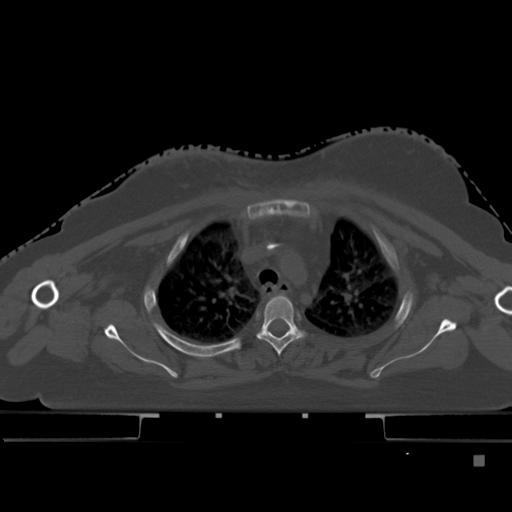
CT including the spine, one axial slice. Position 346 of 495 along the scan axis. Bone window (W 1800 / L 400 HU). 512 × 512 image matrix, field of view 404 × 404 mm. Patient: female, 33 years. From the clinical record (not read from this slice): primary cancer: breast; vertebrae with lytic lesions (as recorded): T1.
Annotated regions visible in this slice (semi-automatic segmentation, software-assisted and operator-edited):
- T3 vertebra: box from (x=258, y=294) to (x=302, y=356) px